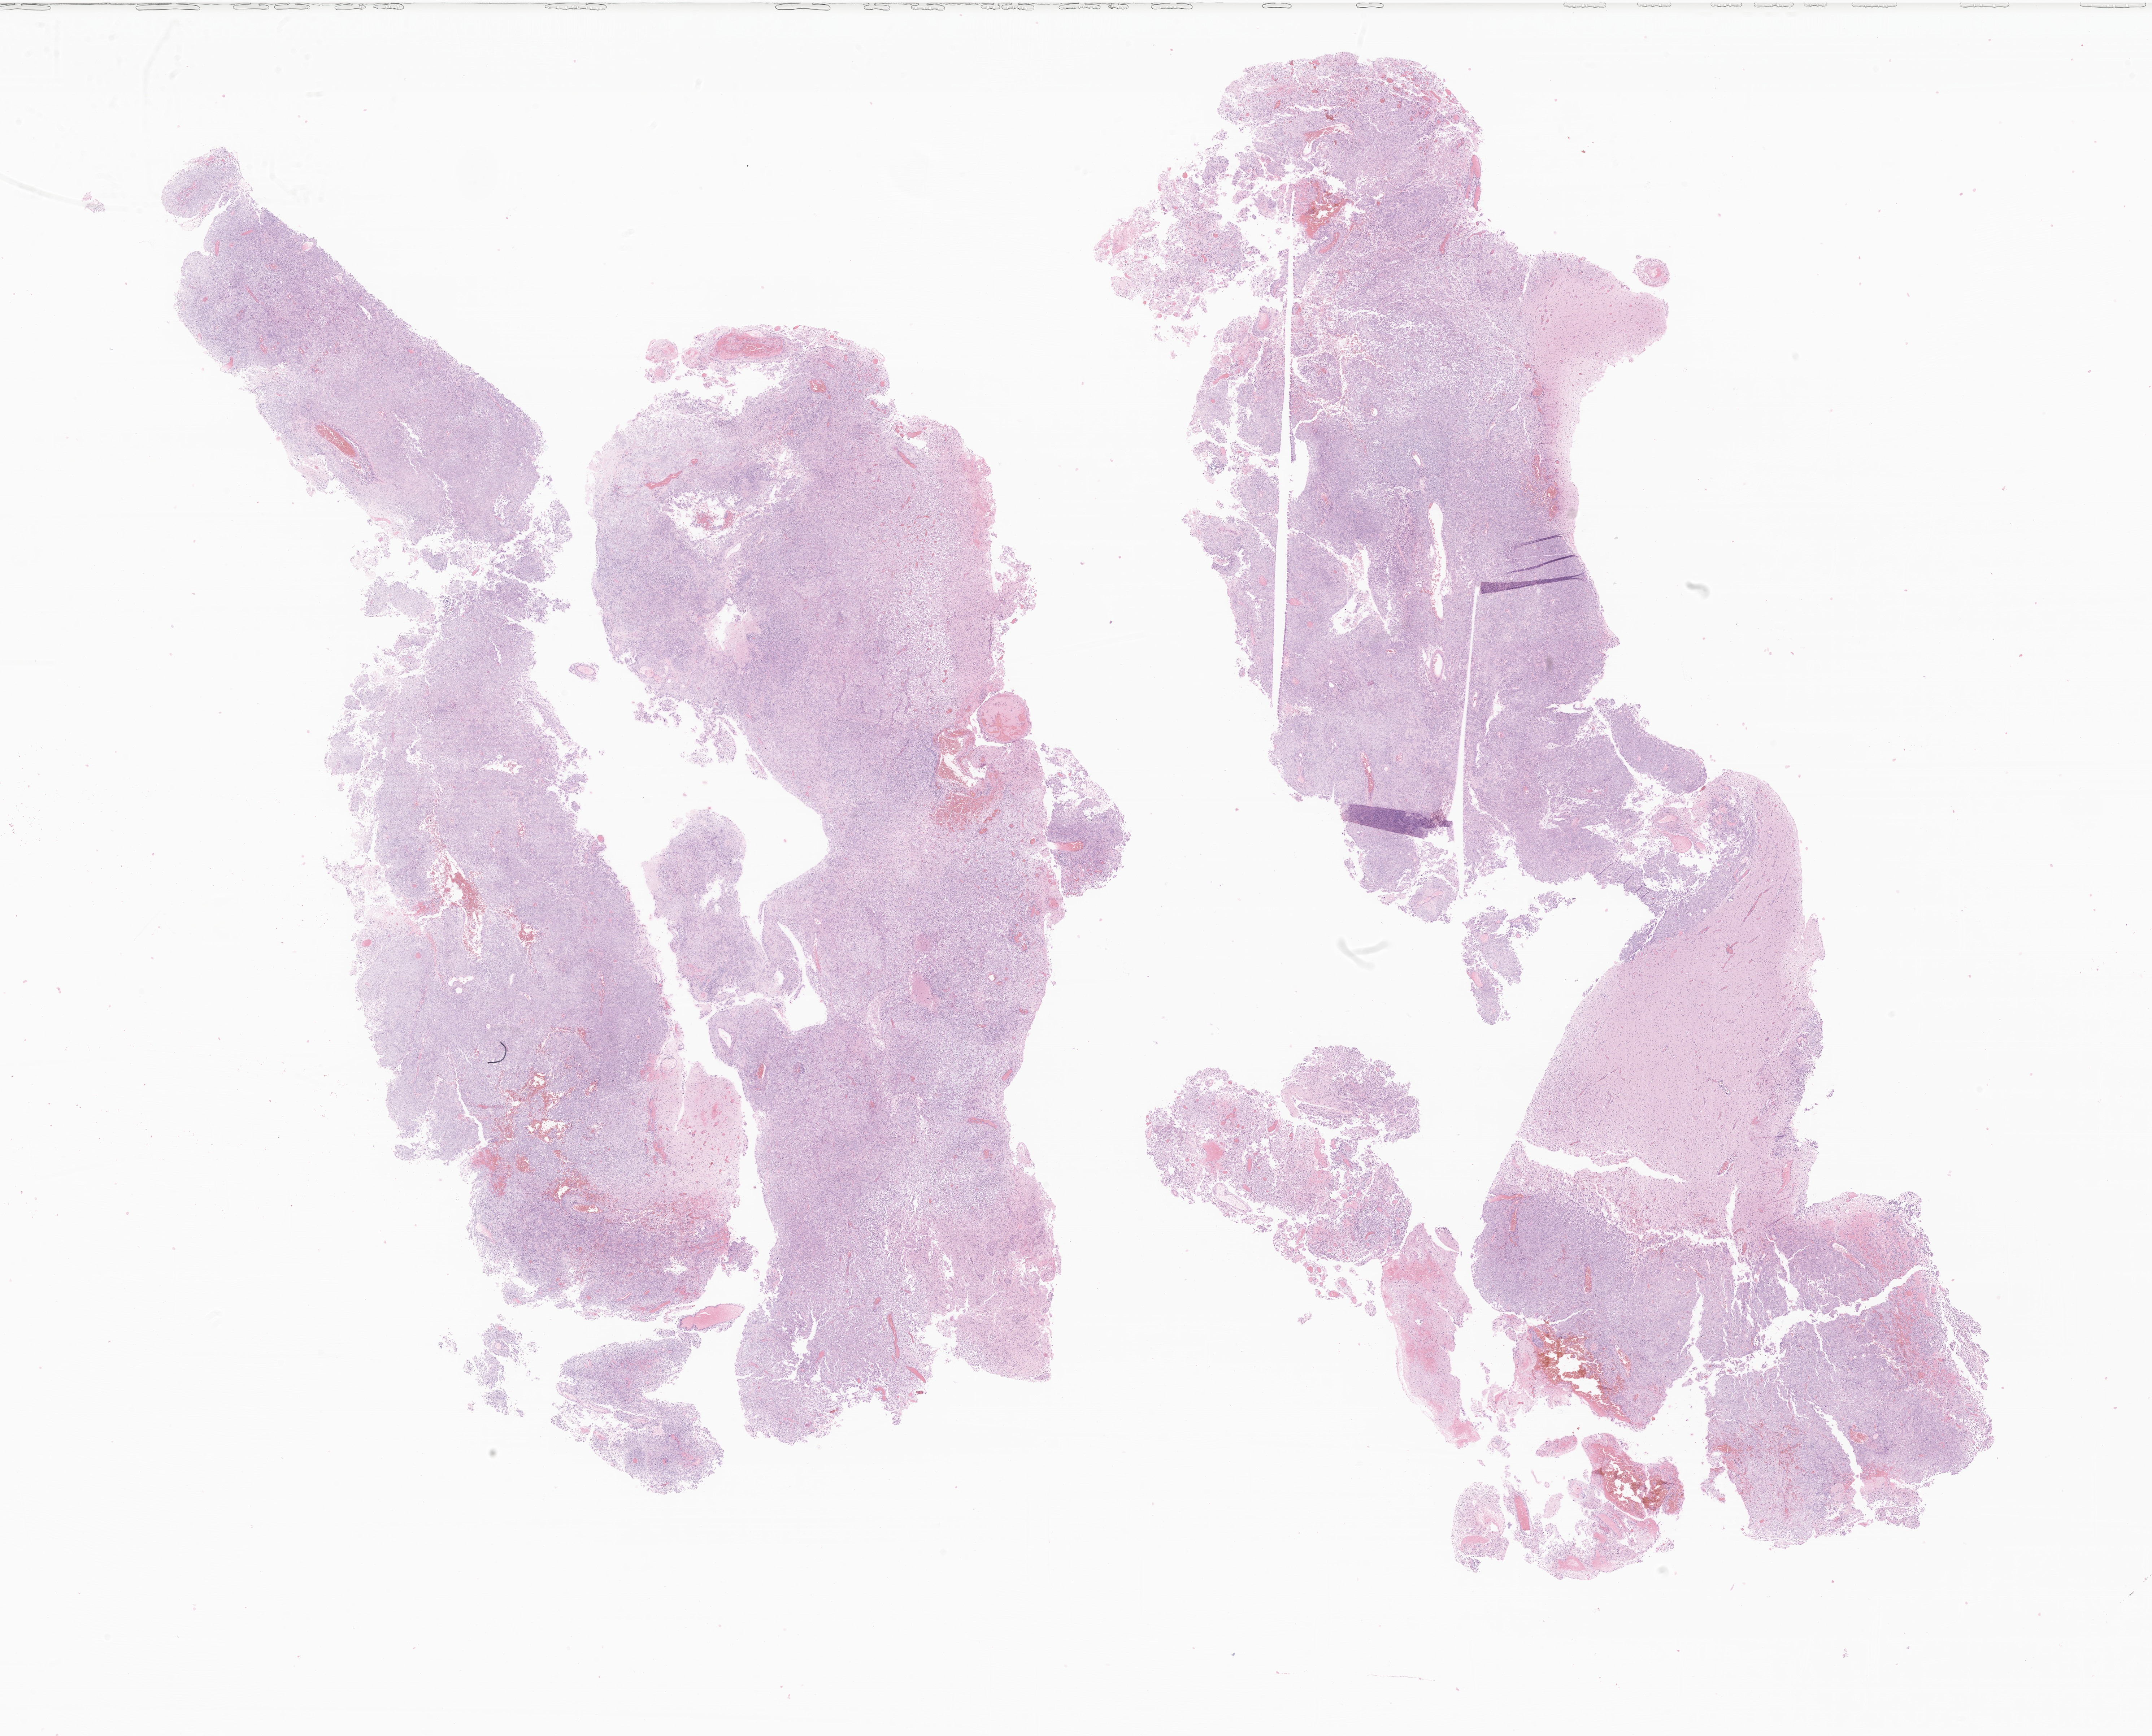
Digitized hematoxylin and eosin (H&E)-stained section of tumor tissue from the brain — whole scanned area (about 25.1 x 20.3 mm) shown as a low-resolution overview, formalin-fixed paraffin-embedded section. Patient female; age 296 days.
Diagnosis (ICD-O-3 morphology term): Atypical teratoid/rhabdoid tumor.